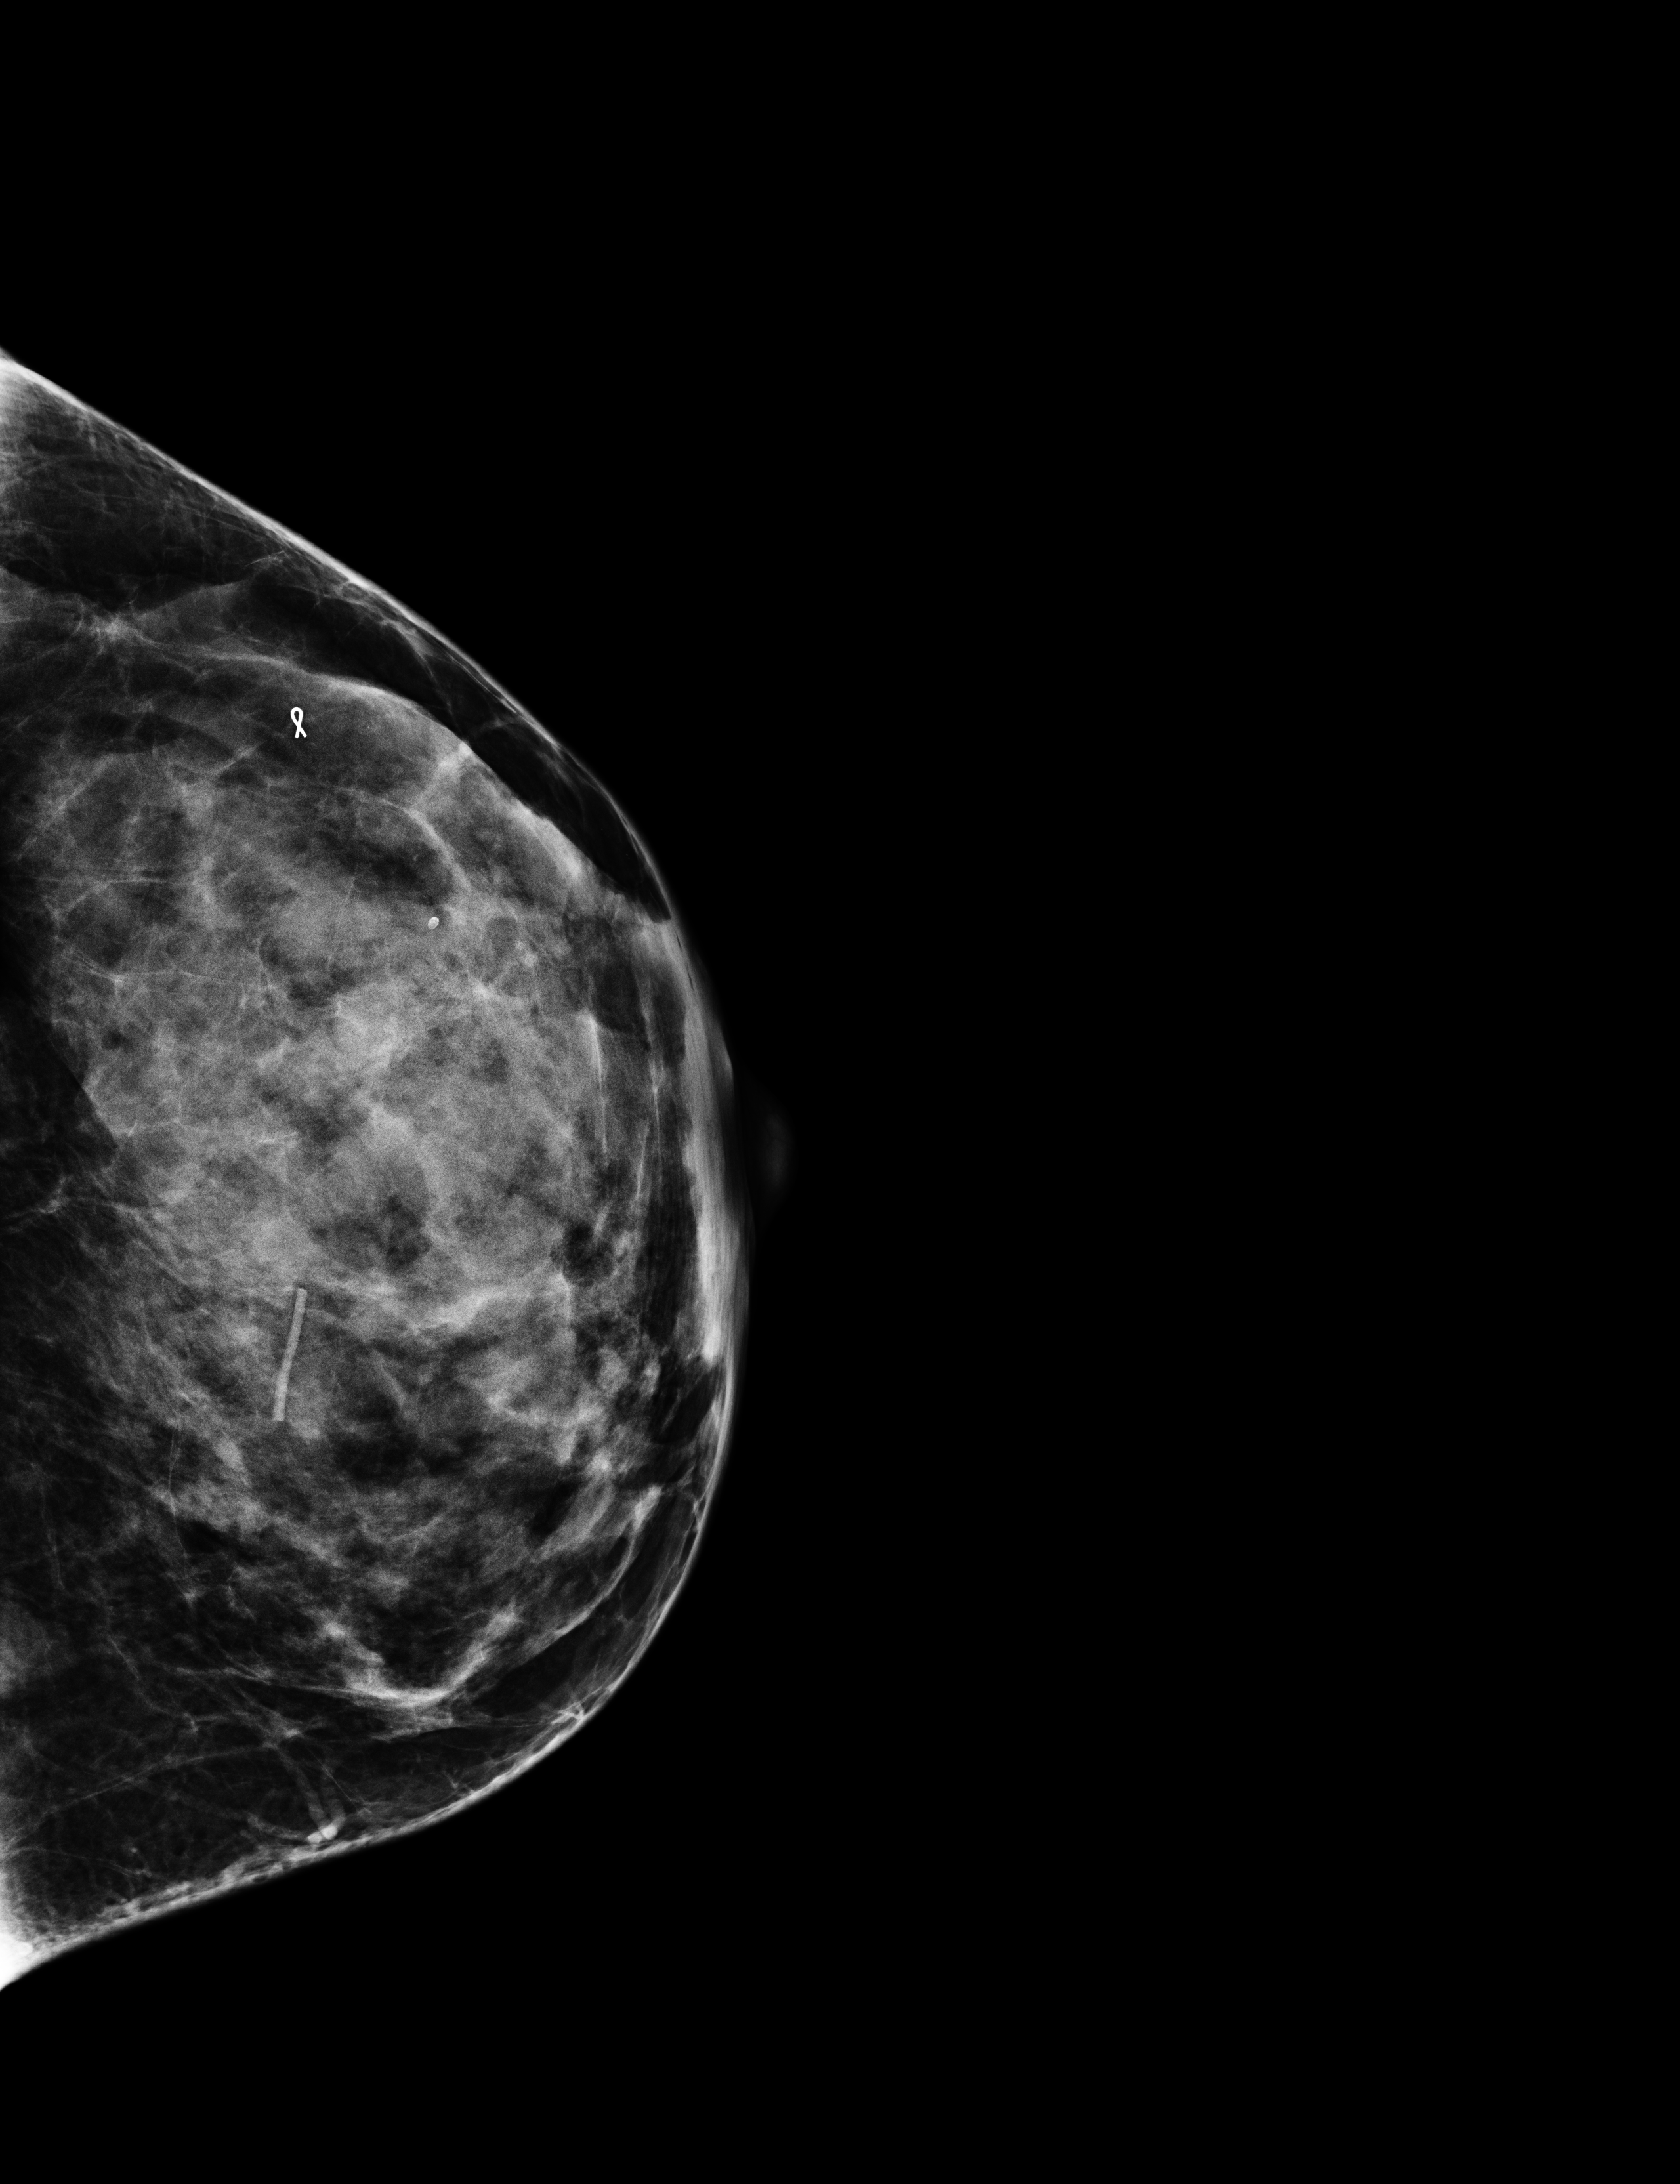
Full-field digital mammogram (FFDM), left breast, cranio-caudal projection, screening examination. Female patient, age 47 years.
Breast density at the screening exam (both breasts): heterogeneously dense (BI-RADS density category c). Final BI-RADS assessment for this screening round (tomosynthesis exam, both breasts): category 4. Recall: recalled for additional imaging after this screen.